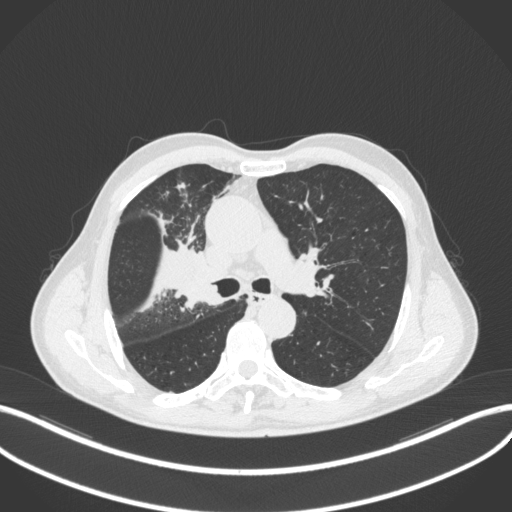
Chest CT, one axial slice; slice 312 of 490 in the series (ordered by position); 120 kVp; lung window (W 1500 / L -600 HU); 1 mm slice thickness; 512 × 512 image matrix. Patient: male, 69 years. Case-level facts recorded for this patient, not image findings: clinical TNM (as recorded): T2a N0 M0.
Outlined on this slice (bounding box drawn by a radiologist):
- lung tumour (recorded histology: adenocarcinoma): box from (x=170, y=261) to (x=221, y=309) px